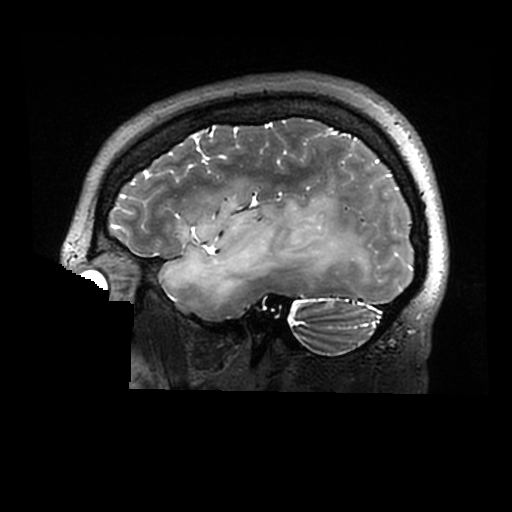
Brain MRI from a brain-tumour surgery series, one sagittal slice. Slice 222 of 320 in the series (ordered by position). 0.6 mm slice thickness. 512 × 512 image matrix, field of view 240 × 240 mm. Case-level facts recorded for this patient, not image findings: histopathology: Astrocytoma; WHO grade: 2; IDH mutation: yes.
Annotated regions visible in this slice (manually delineated by an expert):
- tumour: bounding box [x1, y1, x2, y2] px = [160, 194, 379, 306]